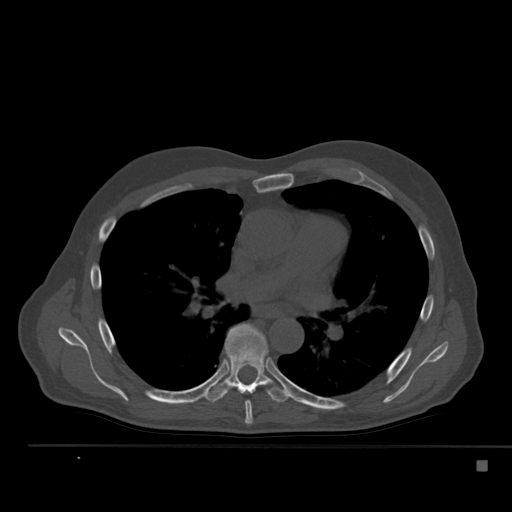
CT including the spine, one axial slice; position 335 of 517 along the scan axis; 120 kVp; bone window (W 1800 / L 400 HU); 1.5 mm slice thickness; 512 × 512 image matrix, field of view 408 × 408 mm. Male patient, age 70 years. From the clinical record (not read from this slice): primary cancer: renal.
Annotated regions visible in this slice (semi-automatically segmented with operator editing):
- T6 vertebra: box from (x=245, y=401) to (x=253, y=425) px
- T7 vertebra: (x=203, y=323)–(x=292, y=403)